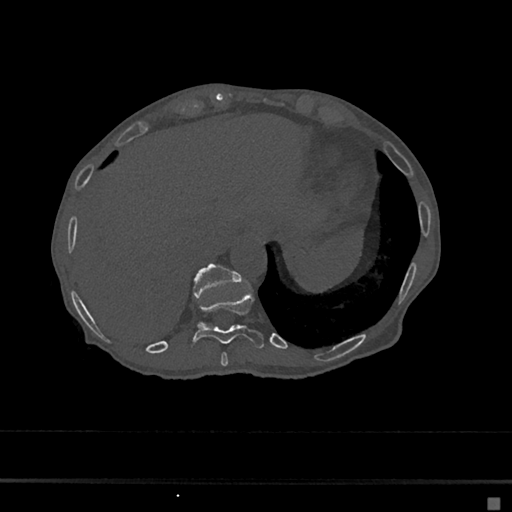
CT including the spine, one axial slice; slice 217 of 797 in the series (ordered by position); 120 kVp; bone window (W 1800 / L 400 HU); 0.5 mm slice thickness; 512 × 512 image matrix. Patient: female, 68 years. From the clinical record (not read from this slice): primary cancer: renal.
Annotated regions visible in this slice (semi-automatically segmented with operator editing):
- T10 vertebra: bounding box <190,290,265,348> (left, top, right, bottom; pixels)
- T11 vertebra: <193,263,241,298>
- T9 vertebra: <220,352,228,367>